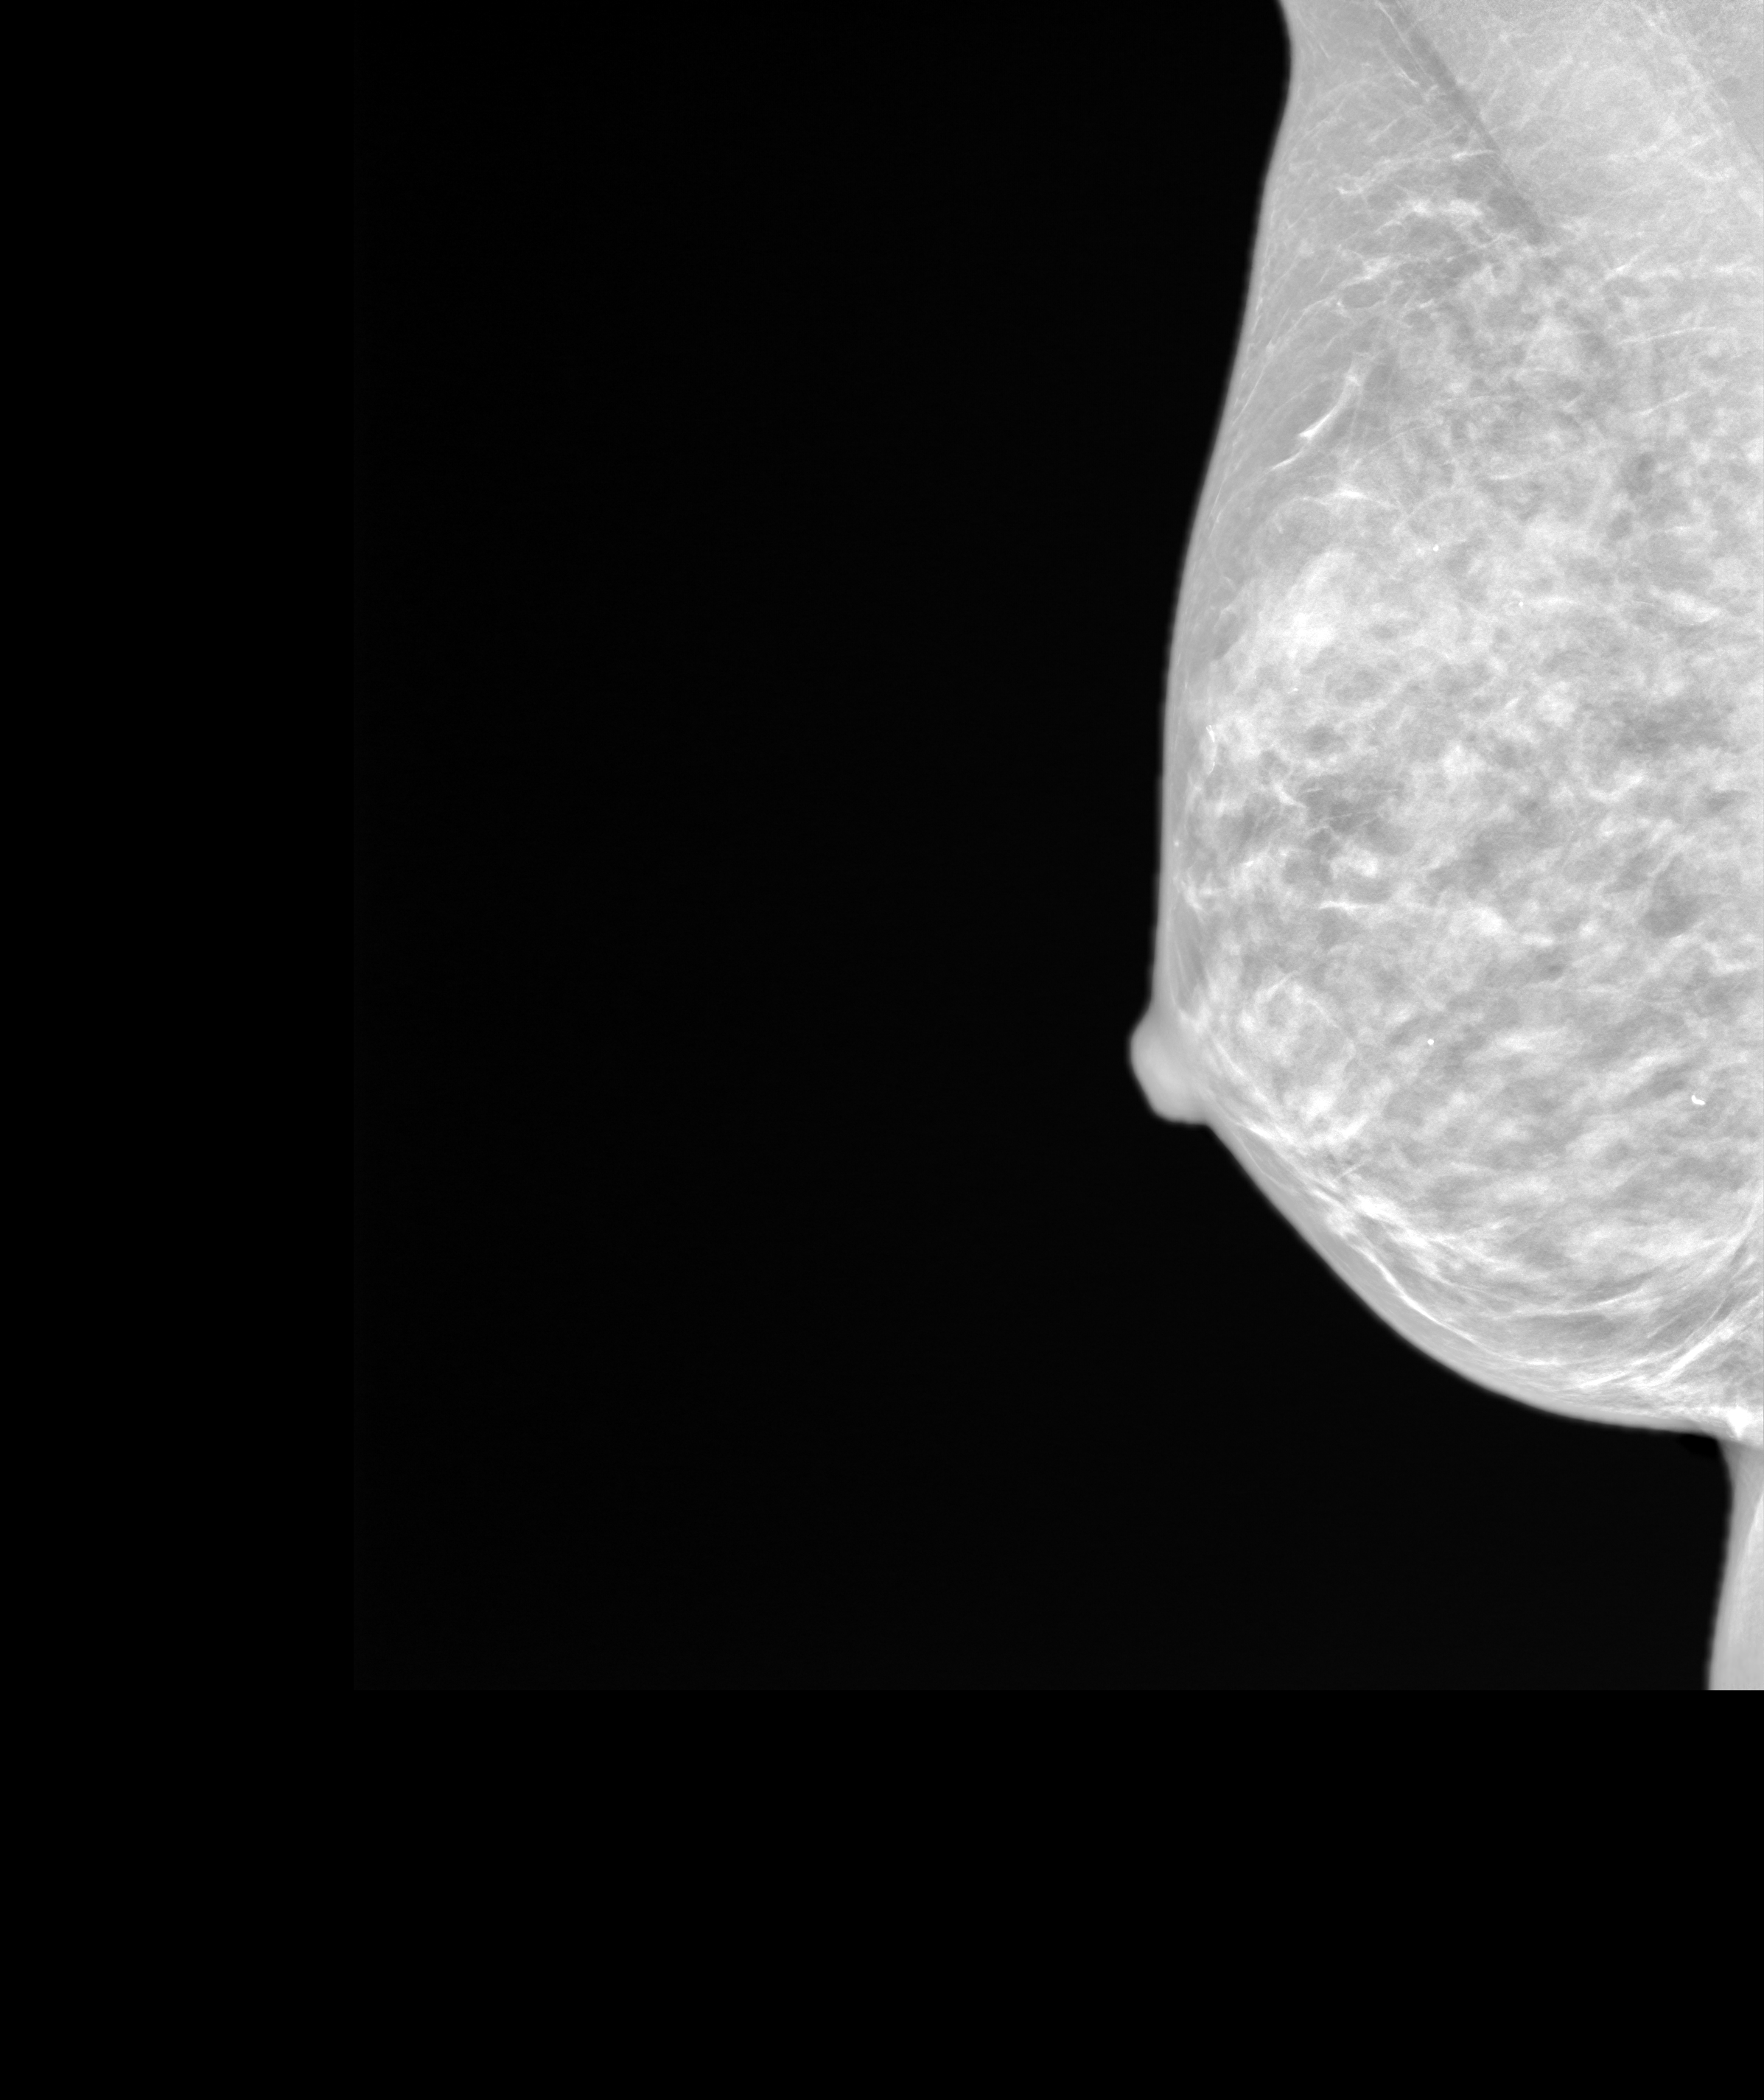
Annual screening mammography examination. Patient: female, 74 years.
Image type: synthesized 2-D view from tomosynthesis. Breast: right. Projection: medio-lateral oblique projection.